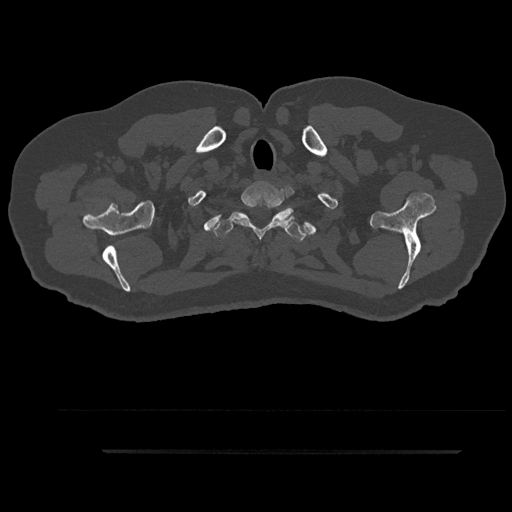
CT including the spine, one axial slice. Slice 783 of 797 in the series (ordered by position). Reconstruction kernel Br40s/3. 120 kVp. Bone window (W 1800 / L 400 HU). 0.5 mm slice thickness. 512 × 512 image matrix. Patient: male, 63 years. From the clinical record (not read from this slice): primary cancer: renal; vertebrae with lytic lesions (as recorded): T8.
Structures marked on this image (semi-automatic segmentation, software-assisted and operator-edited):
- T1 vertebra: bounding box <231,185,293,238> (left, top, right, bottom; pixels)
- T2 vertebra: <213,206,306,241>